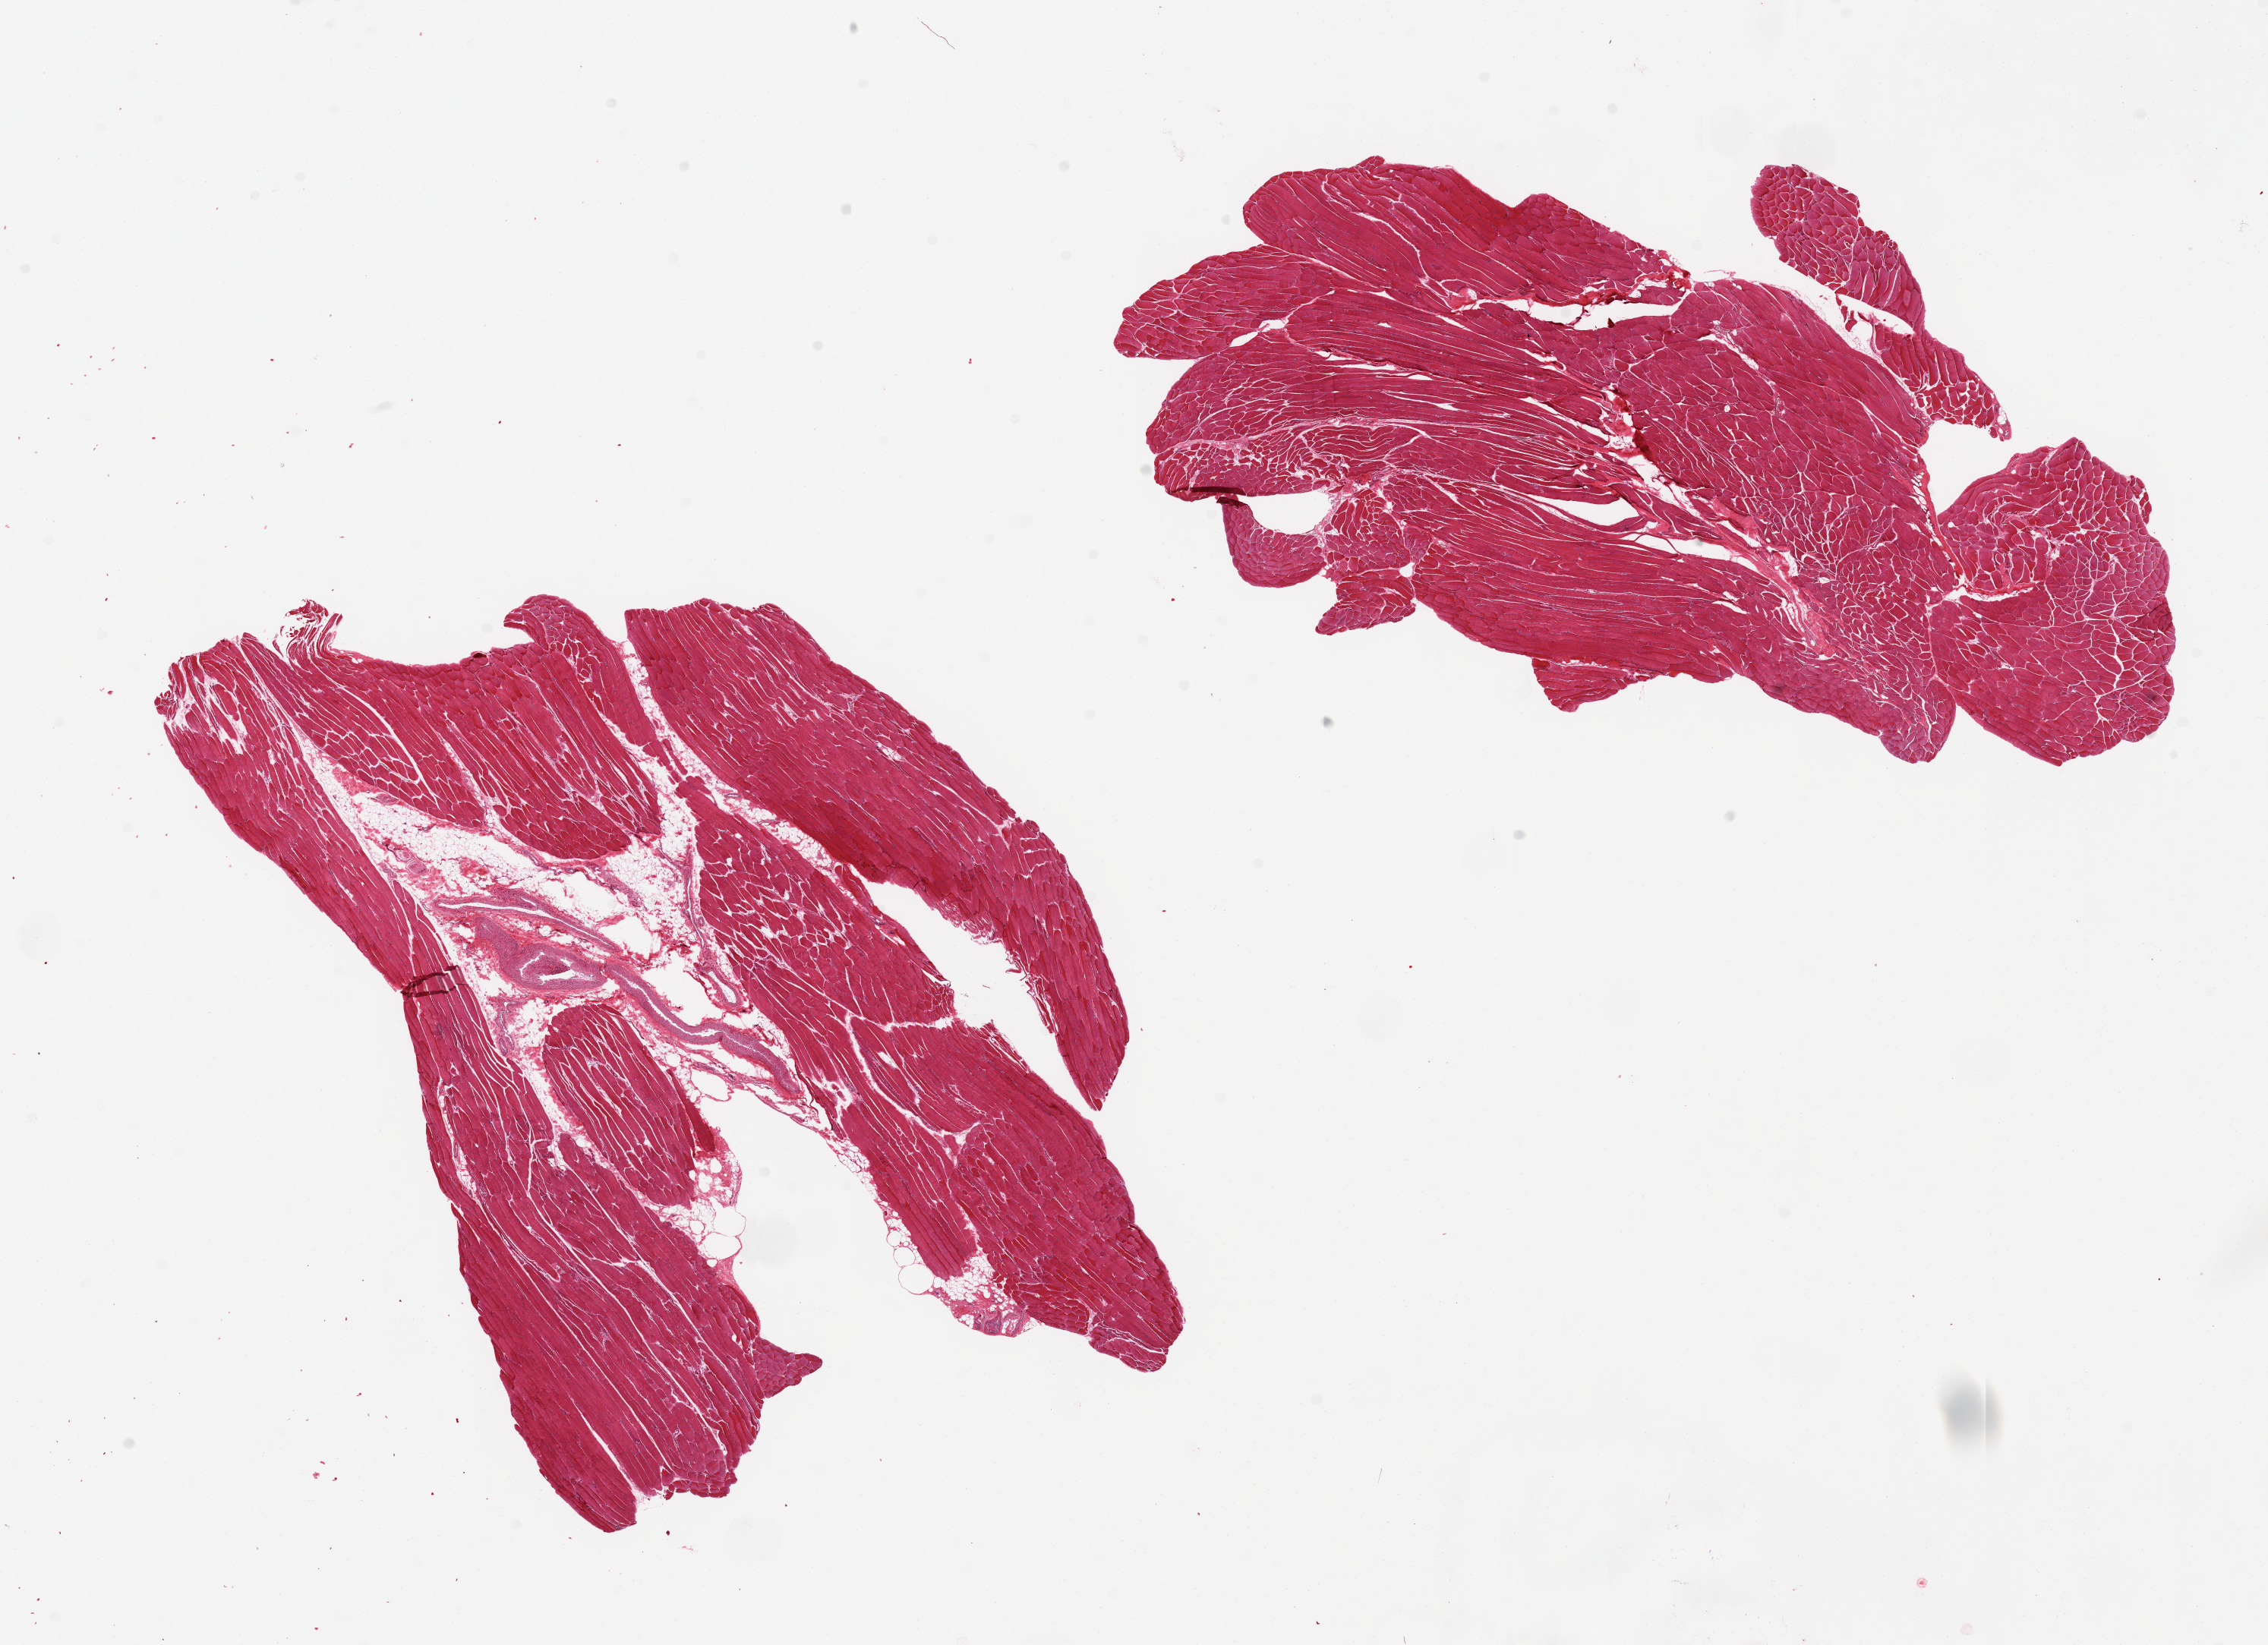
Whole-slide image, H&E stain, brightfield — a low-resolution overview of the entire scanned area, about 23.6 x 17.1 mm (acquisition: 20x scan). PAXgene-fixed paraffin-embedded (PFPE) section. Section of skeletal muscle (target tissue). Tissue donor sample. Donor sex: male.
• reviewer comment on this tissue sample: 2 pieces, one piece is 10-20% internal fat/vessels